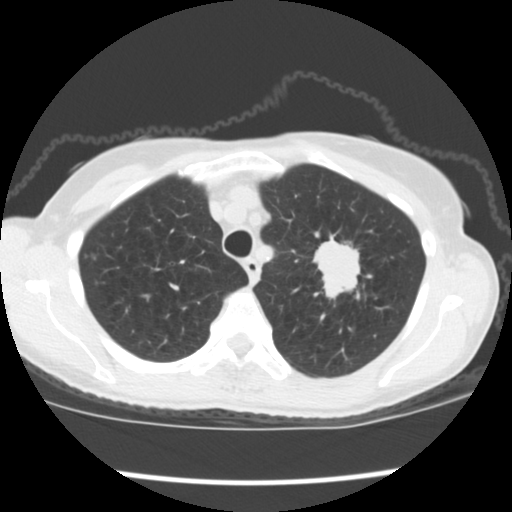
Chest CT (low-dose screening protocol), one axial image, baseline screening round, lung window (W 1500 / L -600 HU), standard (soft-tissue) reconstruction kernel (STANDARD), slice 32 of 176 in the series, 512 × 512 image matrix, field of view 318 × 318 mm. Female participant, aged 67 years at enrolment. Former smoker at enrolment.
Expert-annotated lung lesion, bounding box [x1, y1, x2, y2] px = [304, 235, 377, 310]. Screening reader's record for this exam (one nodule recorded; not confirmed to be the boxed lesion): non-calcified nodule or mass ≥4 mm, left upper lobe, 34 × 32 mm, spiculated (stellate) margins, soft tissue attenuation, pre-existing on the prior screen: no. Official screen result: positive, change unspecified: nodule(s) >= 4 mm or enlarging nodule(s), mass(es), or other non-specific abnormalities suspicious for lung cancer. Lung cancer was diagnosed 17 days after this screen: small cell carcinoma, NOS, left upper lobe, stage IIIA (AJCC 6th edition), 40 mm at pathology.